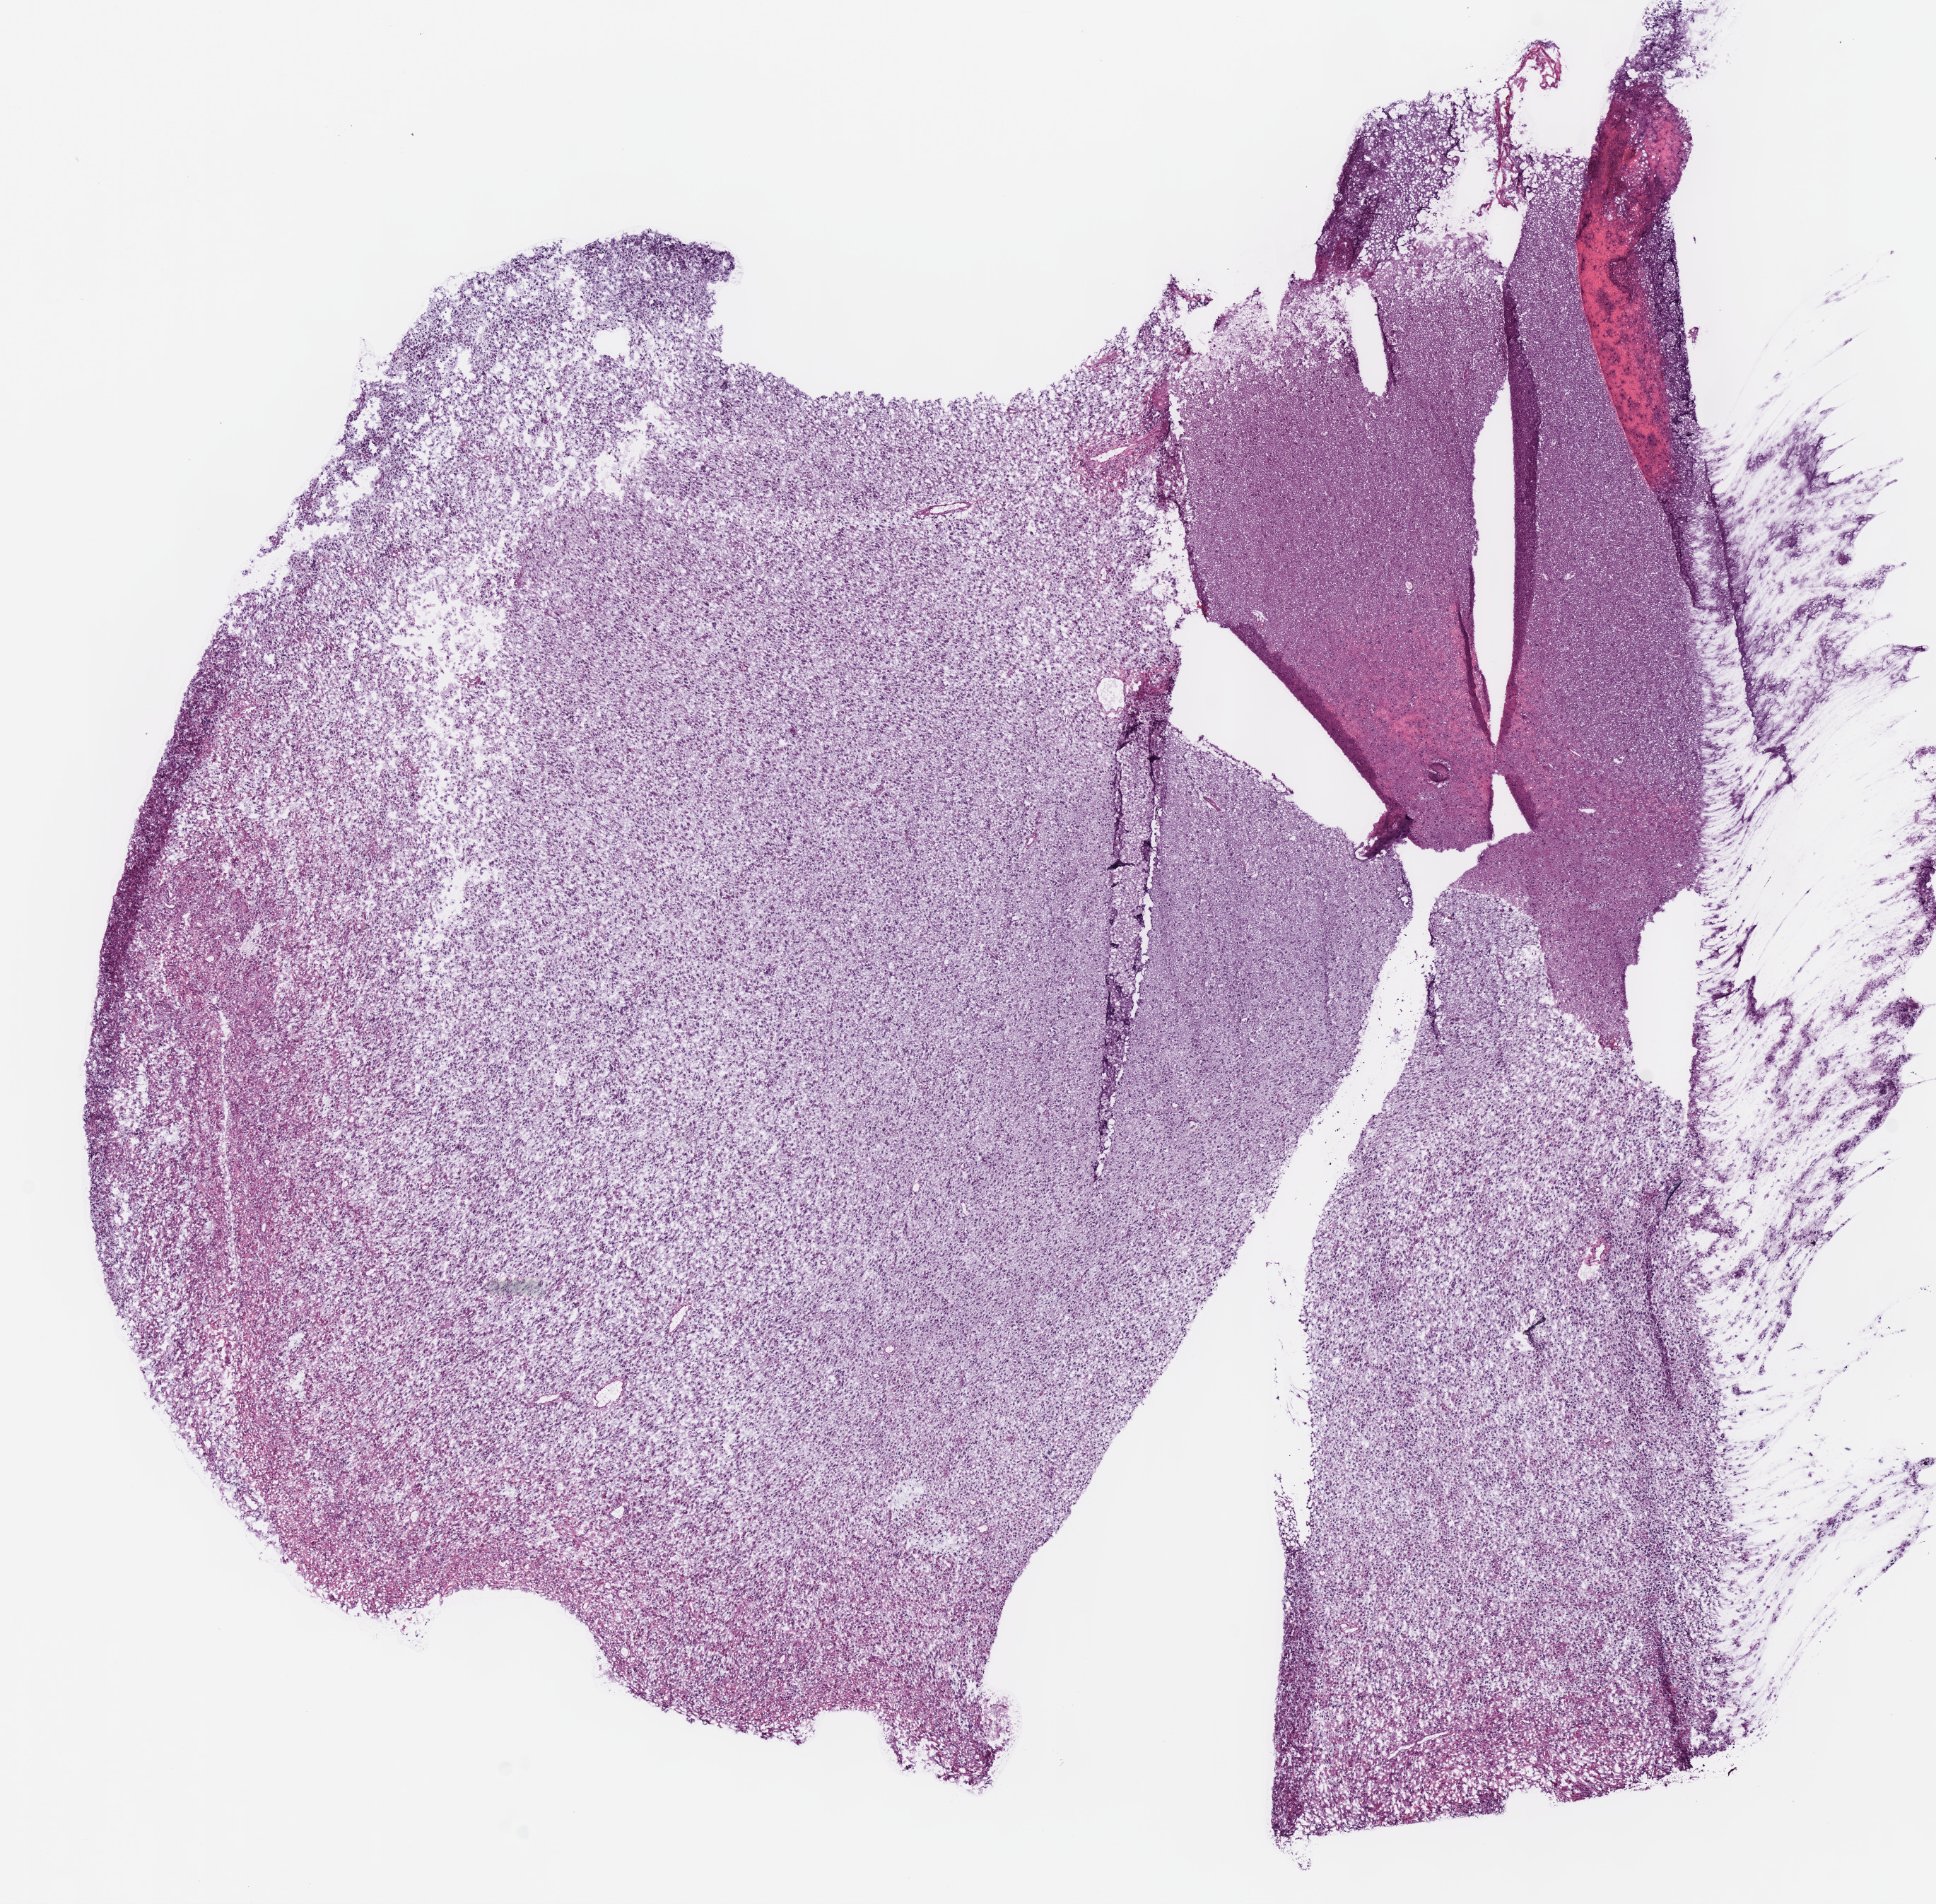
Hematoxylin and eosin (H&E) stained whole-slide image, shown as a low-resolution overview of the whole scanned area (about 10.8 x 10.6 mm, from a 40x scan), frozen section from the bottom of the tissue portion, sample: primary tumour, brain. Male patient; age at initial diagnosis 29 years. Composition of this section per pathologist review: tumour cells 85%, tumour nuclei 85%.
Diagnosis: Mixed glioma (cerebrum).